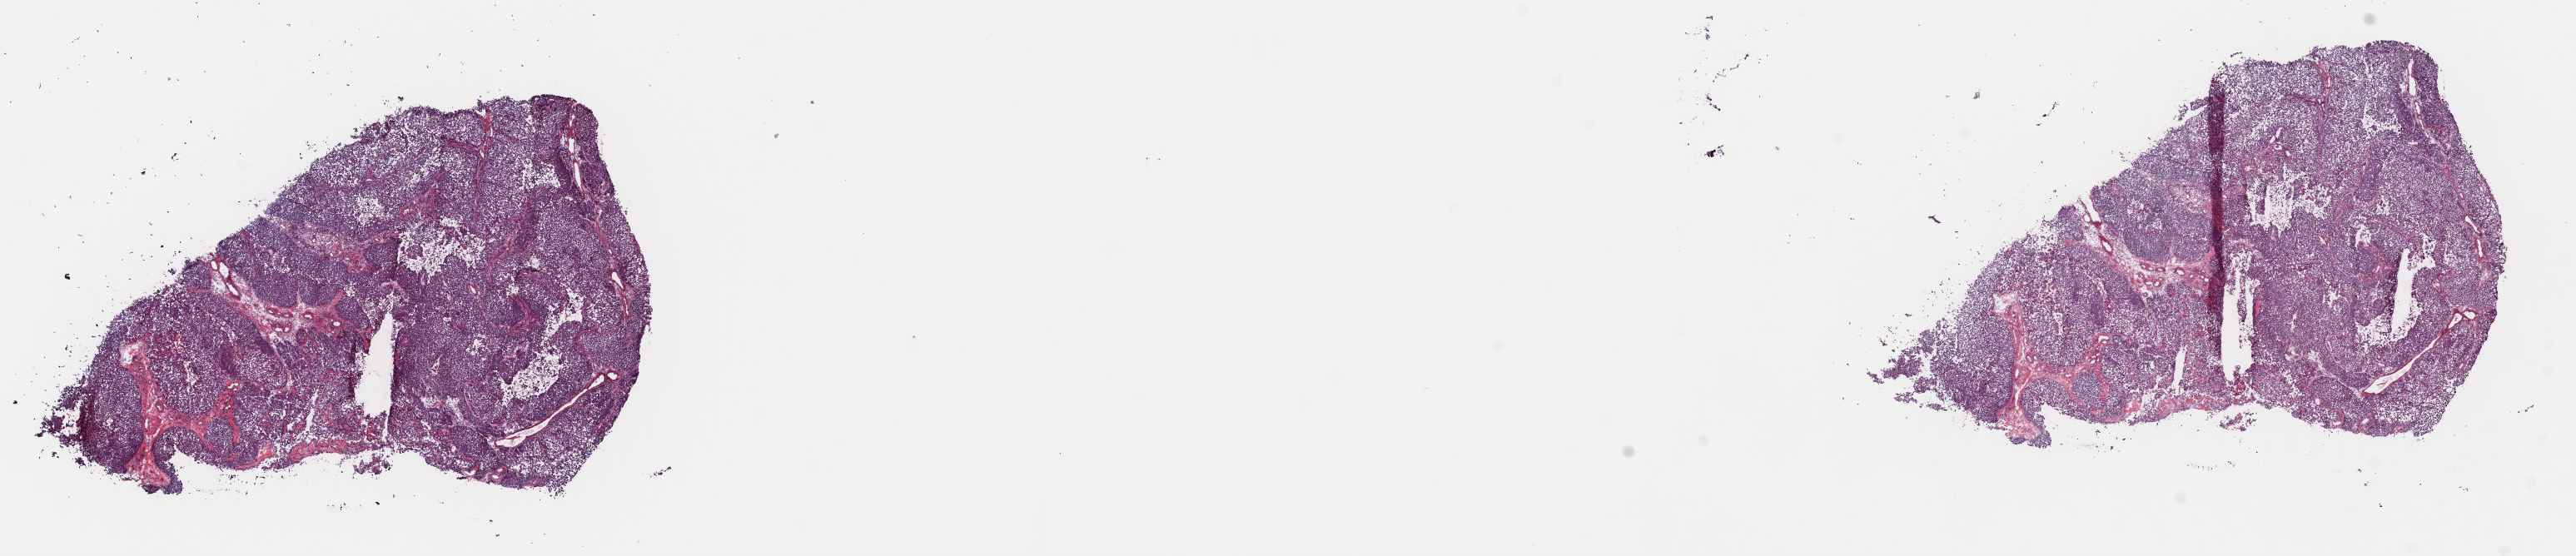
Whole-slide histology image, H&E, a low-resolution overview of the entire scanned area, about 24.4 x 5.3 mm (slide scanned at 40x), frozen section from the top of the tissue portion, primary tumour sample from the bladder. Male, age 81 years at initial diagnosis. Histologic grade: low grade. Slide review estimates, as recorded: tumour cells 72%, tumour nuclei 90%, normal cells 0%, stromal cells 25%, necrosis 3%. Inflammatory infiltration, as recorded: lymphocyte infiltration 3%, monocyte infiltration 0%, neutrophil infiltration 0%.
Pathologic diagnosis: Transitional cell carcinoma. AJCC pathologic stage: II (7th edition).